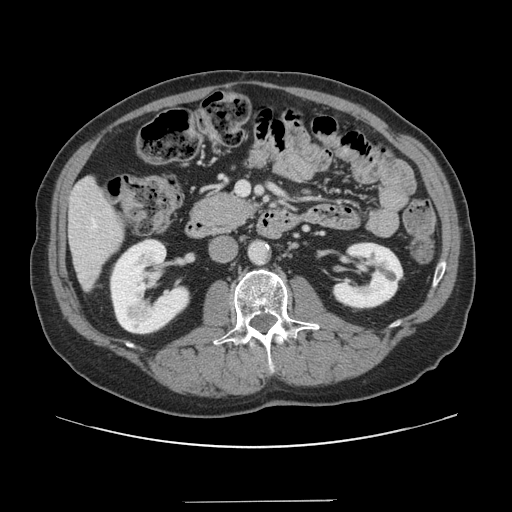
Contrast-enhanced abdominal CT, one axial slice. Position 51 of 151 along the scan axis. 120 kVp. Soft-tissue window (W 400 / L 40 HU). 2.5 mm slice thickness. 512 × 512 image matrix. Male patient, age 63 years. Case-level facts recorded for this patient, not image findings: diagnosis: colorectal cancer liver metastases, imaged before liver resection; multiple liver metastases: no; largest metastasis: 2.1 cm.
Outlined on this slice (manually delineated by an expert):
- hepatic veins: bounding box [x1, y1, x2, y2] px = [93, 220, 97, 228]
- liver: [70, 179, 124, 287]
- planned liver remnant (the part of the liver to remain after resection): [70, 179, 124, 288]
- portal vein (with intrahepatic branches): [237, 182, 249, 195]